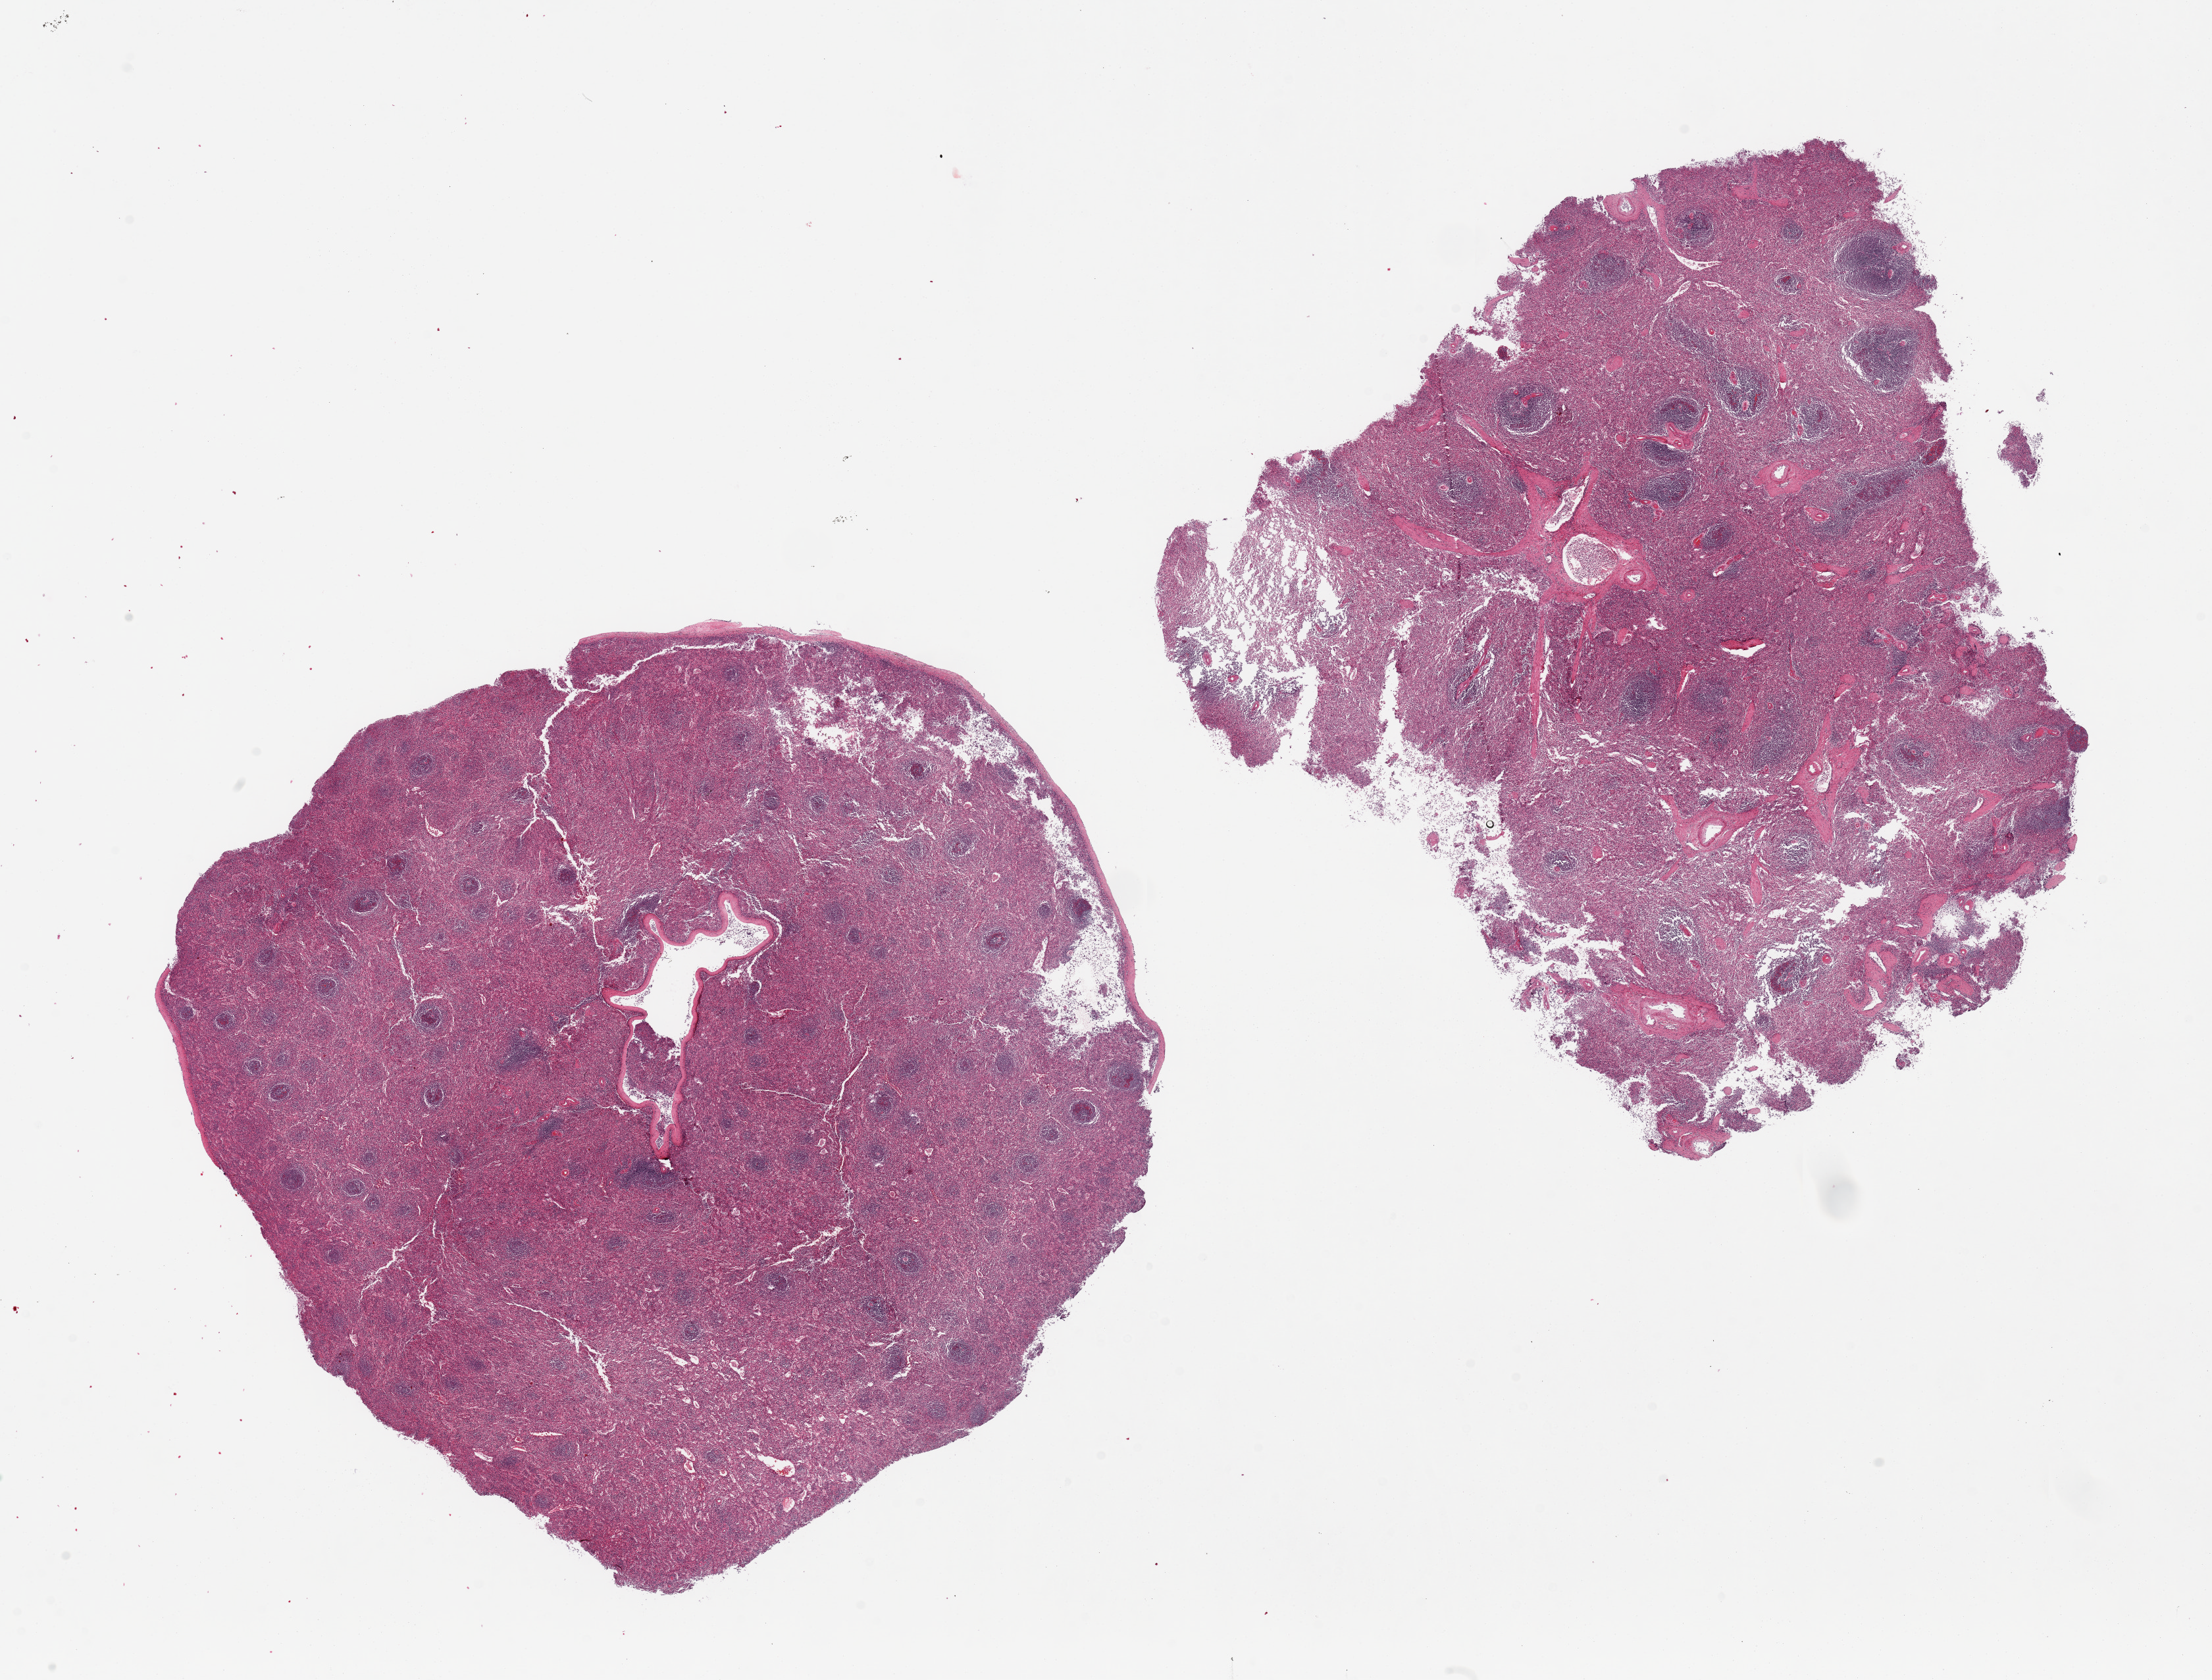
Haematoxylin and eosin whole-slide image, whole scanned area (about 26.6 x 20.2 mm, slide scanned at 20x) shown as a low-resolution overview, PAXgene-fixed paraffin-embedded (PFPE) section, target tissue: spleen, tissue donor sample.
• pathologist's review note for this sample: 2 pieces, 11x11 & 11x11mm; mild congrestion